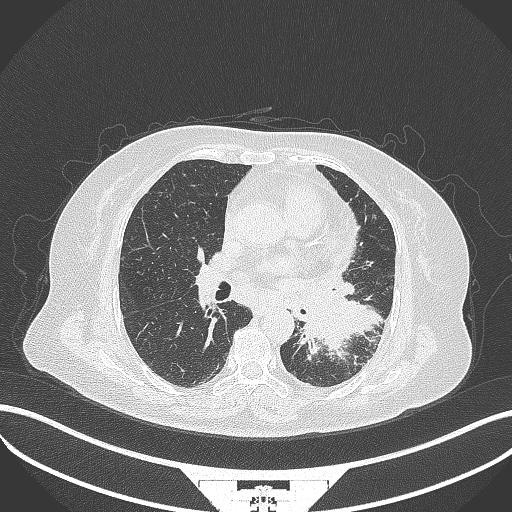
Chest CT, one axial slice; slice 180 of 322 in the series (ordered by position); 120 kVp; lung window (W 1500 / L -600 HU); 1 mm slice thickness; 512 × 512 image matrix, field of view 400 × 400 mm. Patient: female, 69 years. From the clinical record (not read from this slice): clinical TNM (as recorded): T2b N3 M1.
Structures marked on this image (rectangle marked by the reading radiologist):
- lung tumour (recorded histology: adenocarcinoma): bounding box (x1, y1, x2, y2) in pixels: (293, 289, 383, 353)